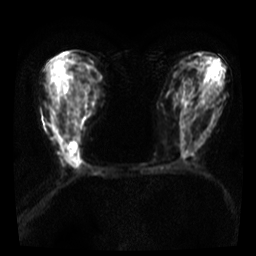
Breast MRI, one axial slice; slice 16 of 36 in the series (ordered by position); diffusion-weighted series; image 2 of 4 stored at this slice position (different b-values; order by instance number); 3 T; 5 mm slice thickness; 256 × 256 image matrix, field of view 300 × 300 mm. Female patient.
Outlined on this slice (manually delineated by an expert):
- tumour on diffusion-weighted imaging: bounding box (x1, y1, x2, y2) in pixels: (68, 142, 77, 154)